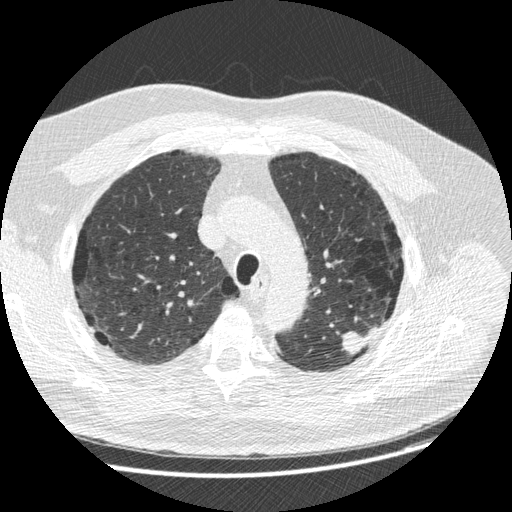
Low-dose screening chest CT, one axial slice. Slice 200 of 258 in the series (ordered by position). Reconstruction kernel STANDARD. 120 kVp. Lung window (W 1500 / L -600 HU). 512 × 512 image matrix, field of view 370 × 370 mm.
Outlined on this slice (outlined manually by an expert reader):
- lesion 1 (tumor, upper lobe of left lung): box from (x=342, y=327) to (x=378, y=355) px